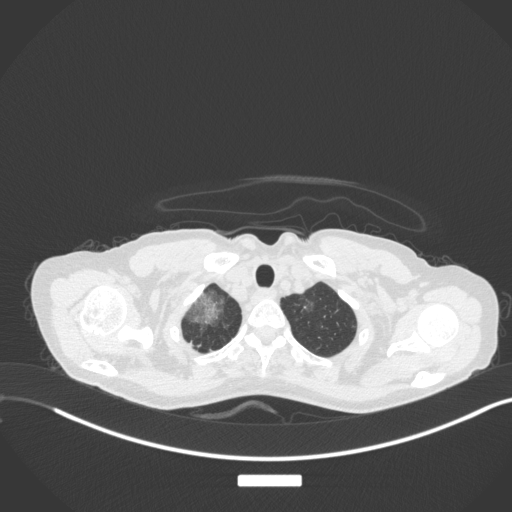
Chest CT, one axial slice. Slice 303 of 311 in the series (ordered by position). Reconstruction kernel B31f. 120 kVp. Lung window (W 1500 / L -600 HU). 1 mm slice thickness. 512 × 512 image matrix, field of view 400 × 400 mm. Patient: female, 59 years. Case-level facts recorded for this patient, not image findings: clinical TNM (as recorded): T3 N0 M0; histopathological grade: G1.
Outlined on this slice (bounding box drawn by a radiologist):
- lung tumour (recorded histology: adenocarcinoma): bounding box (x1, y1, x2, y2) in pixels: (188, 290, 218, 327)